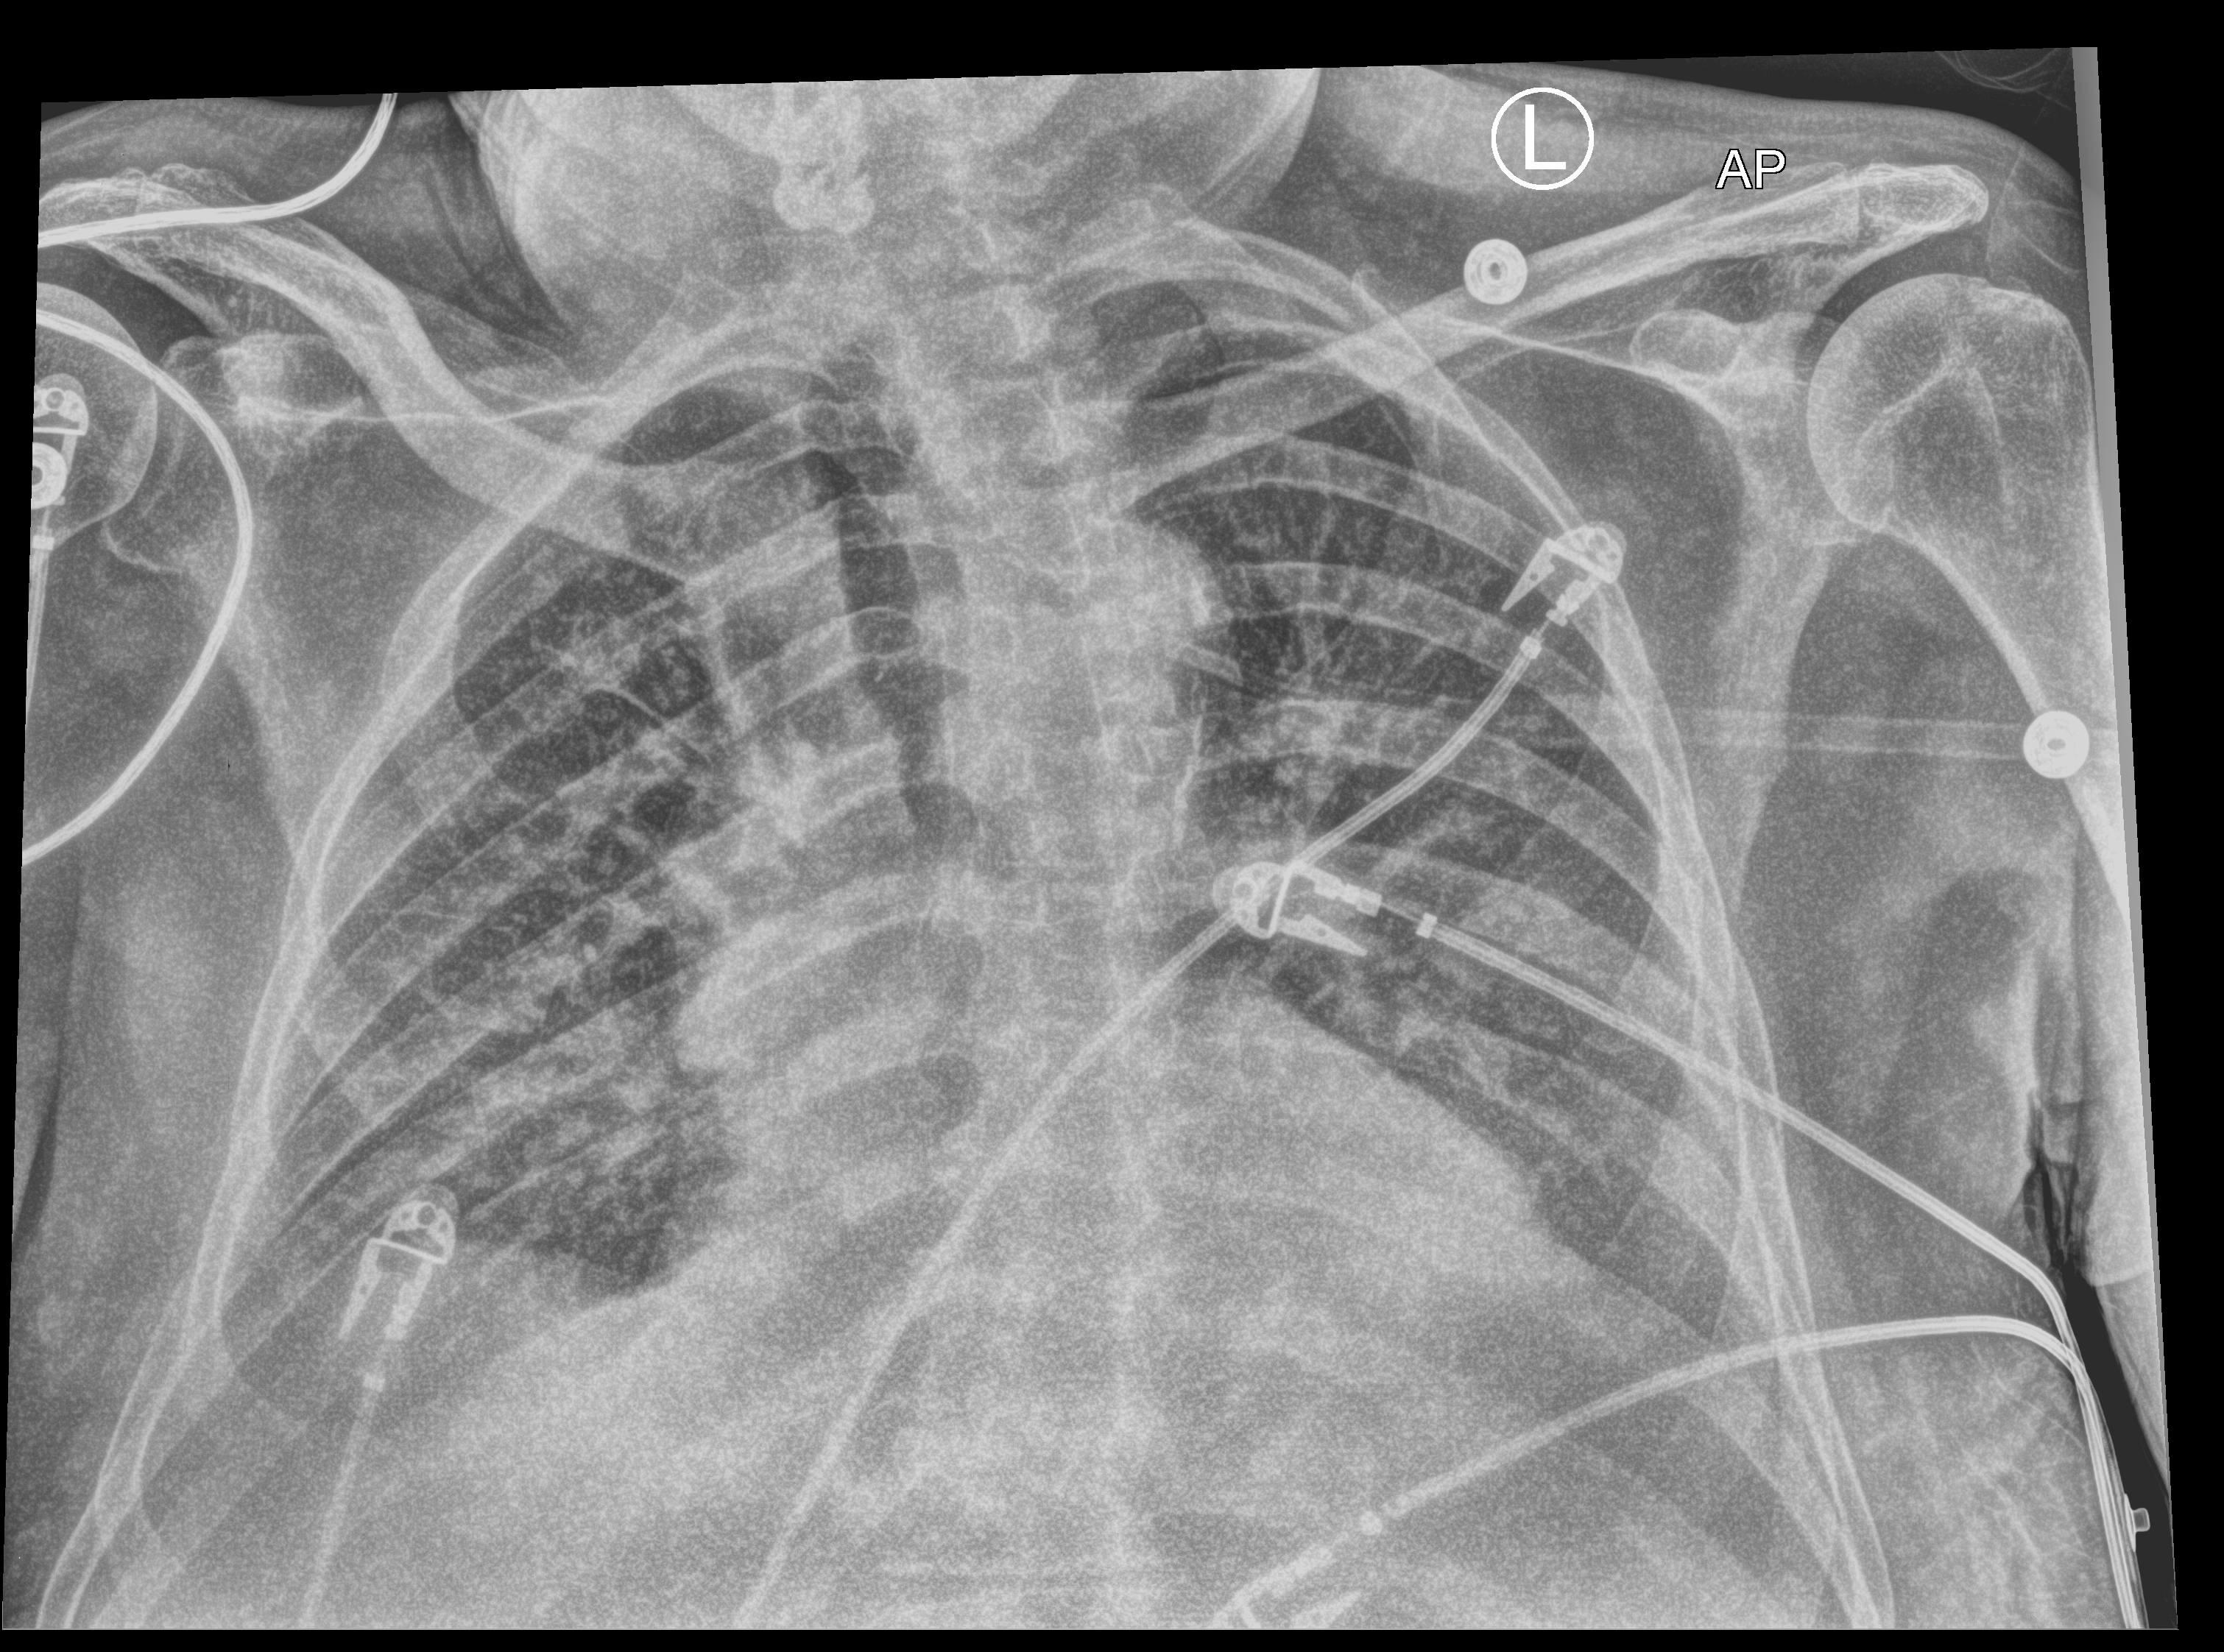
Chest X-ray (portable), anteroposterior (AP) projection. Male patient hospitalised with COVID-19, age 75–90 years.
Hospital-stay facts (about this admission, not read from this image; timing relative to this image not recorded):
- mechanically ventilated during this hospital stay: no
- chronic kidney disease (admission record): no
- length of hospital stay: 17 days